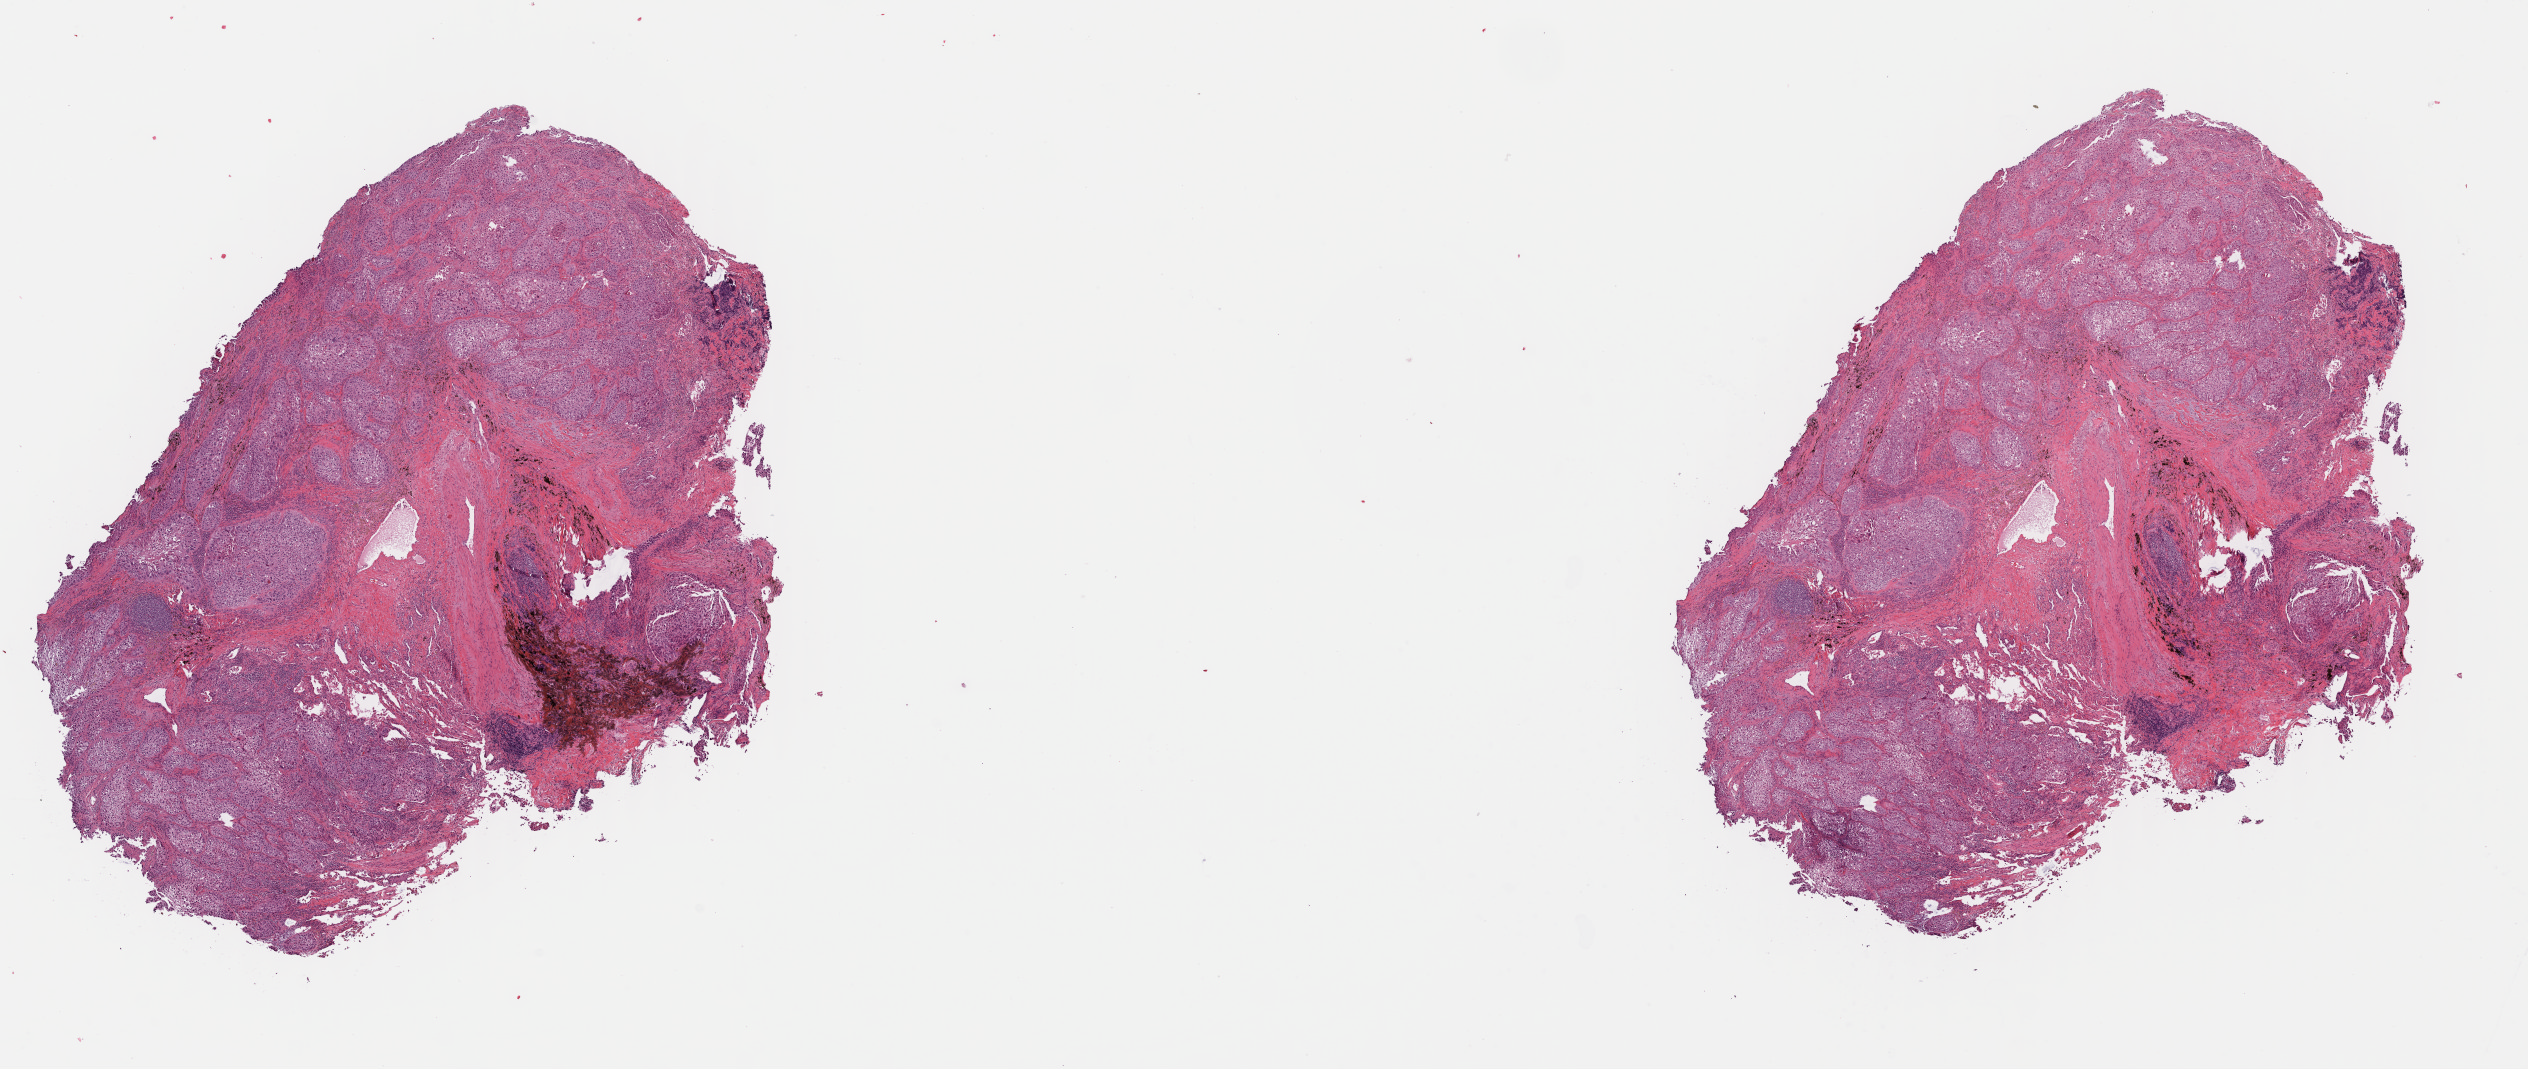
Whole-slide histology image, H&E — whole scanned area (about 19.9 x 8.4 mm, acquisition: 40x scan) shown as a low-resolution overview. FFPE section. Sample: primary tumour, lung. Patient: male, age at initial diagnosis 69 years.
• laterality: left
• AJCC pathologic stage: IB (7th edition)
• diagnosis: Squamous cell carcinoma, NOS (upper lobe, lung)